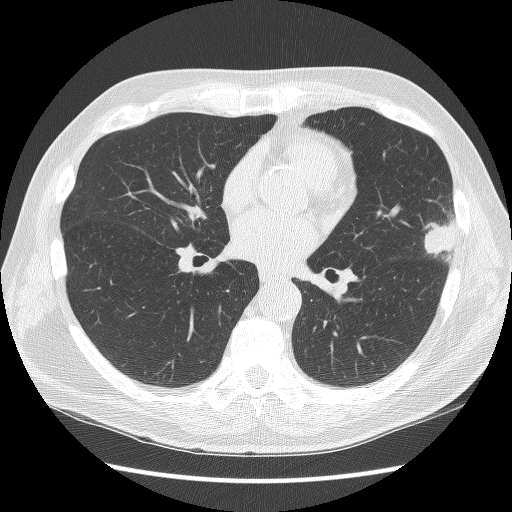
Axial slice from a low-dose chest CT screening exam; third annual screen; lung window (W 1500 / L -600 HU); 2.5 mm slice thickness; slice 66 of 134 in the series. Male participant, aged 67 years at enrolment. Former smoker at enrolment.
Expert reader's lesion annotation, bounding box <408,202,474,274> (left, top, right, bottom; pixels). Reader record for this screening exam (exam-level; its link to the box is not recorded): non-calcified nodule or mass ≥4 mm, left upper lobe, 22 × 17 mm, poorly defined margins, soft tissue attenuation, pre-existing on the prior screen: yes; interval growth: yes. Lung cancer was diagnosed 72 days after this screen: squamous cell carcinoma, NOS, left upper lobe, moderately differentiated (G2), stage IB (AJCC 6th edition), 25 mm at pathology.